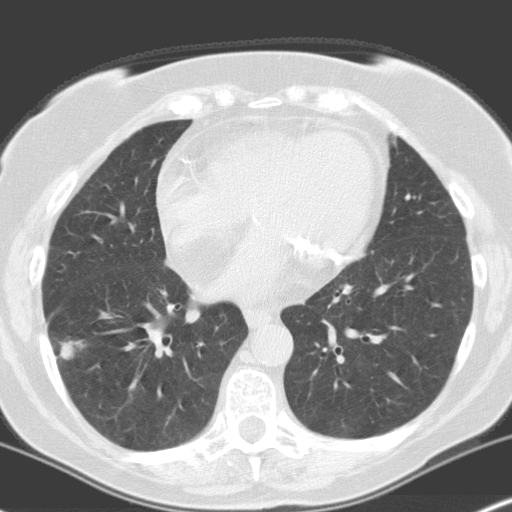
Chest CT (low-dose screening protocol), one axial image; baseline screening round; lung window (W 1500 / L -600 HU); 3.2 mm slice thickness; standard (soft-tissue) reconstruction kernel (C); slice 87 of 160 in the series. Female, age 70 years at enrolment. Current smoker at enrolment.
Expert-annotated lung lesion, bounding box [x1, y1, x2, y2] px = [35, 311, 101, 381]. The screening reader recorded 4 non-calcified nodules or masses ≥4 mm on this exam (right lower lobe, right upper lobe, left upper lobe, left upper lobe); which of them this box marks is not recorded. Later outcome: lung cancer diagnosed 28 days after this screen — adenocarcinoma, NOS, right lower lobe, moderately differentiated (G2), stage IV (AJCC 6th edition), 28 mm at pathology.